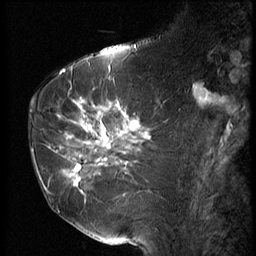
Breast MRI (dynamic contrast-enhanced), one sagittal slice. 3 images stored at this slice position (order not interpretable as contrast timing). 1.5 T. TE 4.2 ms, TR 9 ms. 2.5 mm slice thickness. 256 × 256 image matrix, field of view 180 × 180 mm. Female patient, age 61 years. From the clinical record (not read from this slice): setting: breast cancer imaged before/during neoadjuvant chemotherapy; receptor status: HR-positive, HER2-negative.
Annotated regions visible in this slice (semi-automatically segmented with operator editing):
- analysis volume of interest (the breast-tissue region the enhancement analysis was run in; not a lesion): bounding box [x1, y1, x2, y2] px = [47, 89, 153, 191]
- tumour enhancement mask (voxels above the 140 % enhancement threshold inside the analysis volume of interest): [49, 99, 147, 186]